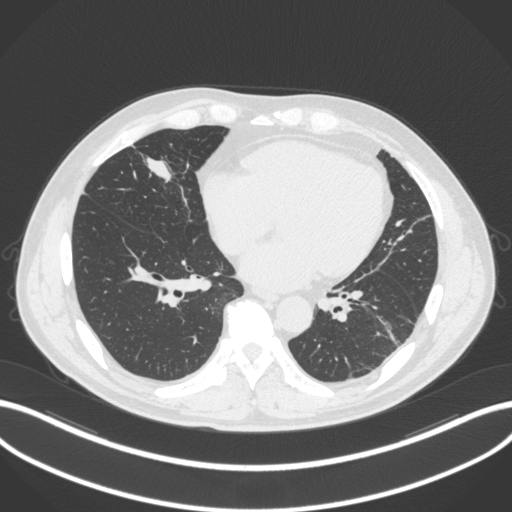
Chest CT, one axial slice; position 101 of 399 along the scan axis; 120 kVp; lung window (W 1500 / L -600 HU); 1 mm slice thickness; 512 × 512 image matrix, field of view 400 × 400 mm. Patient: male, 59 years. From the clinical record (not read from this slice): clinical TNM (as recorded): T2a N1 M0.
Outlined on this slice (rectangle marked by the reading radiologist):
- lung tumour (recorded histology: adenocarcinoma): box from (x=138, y=150) to (x=179, y=193) px